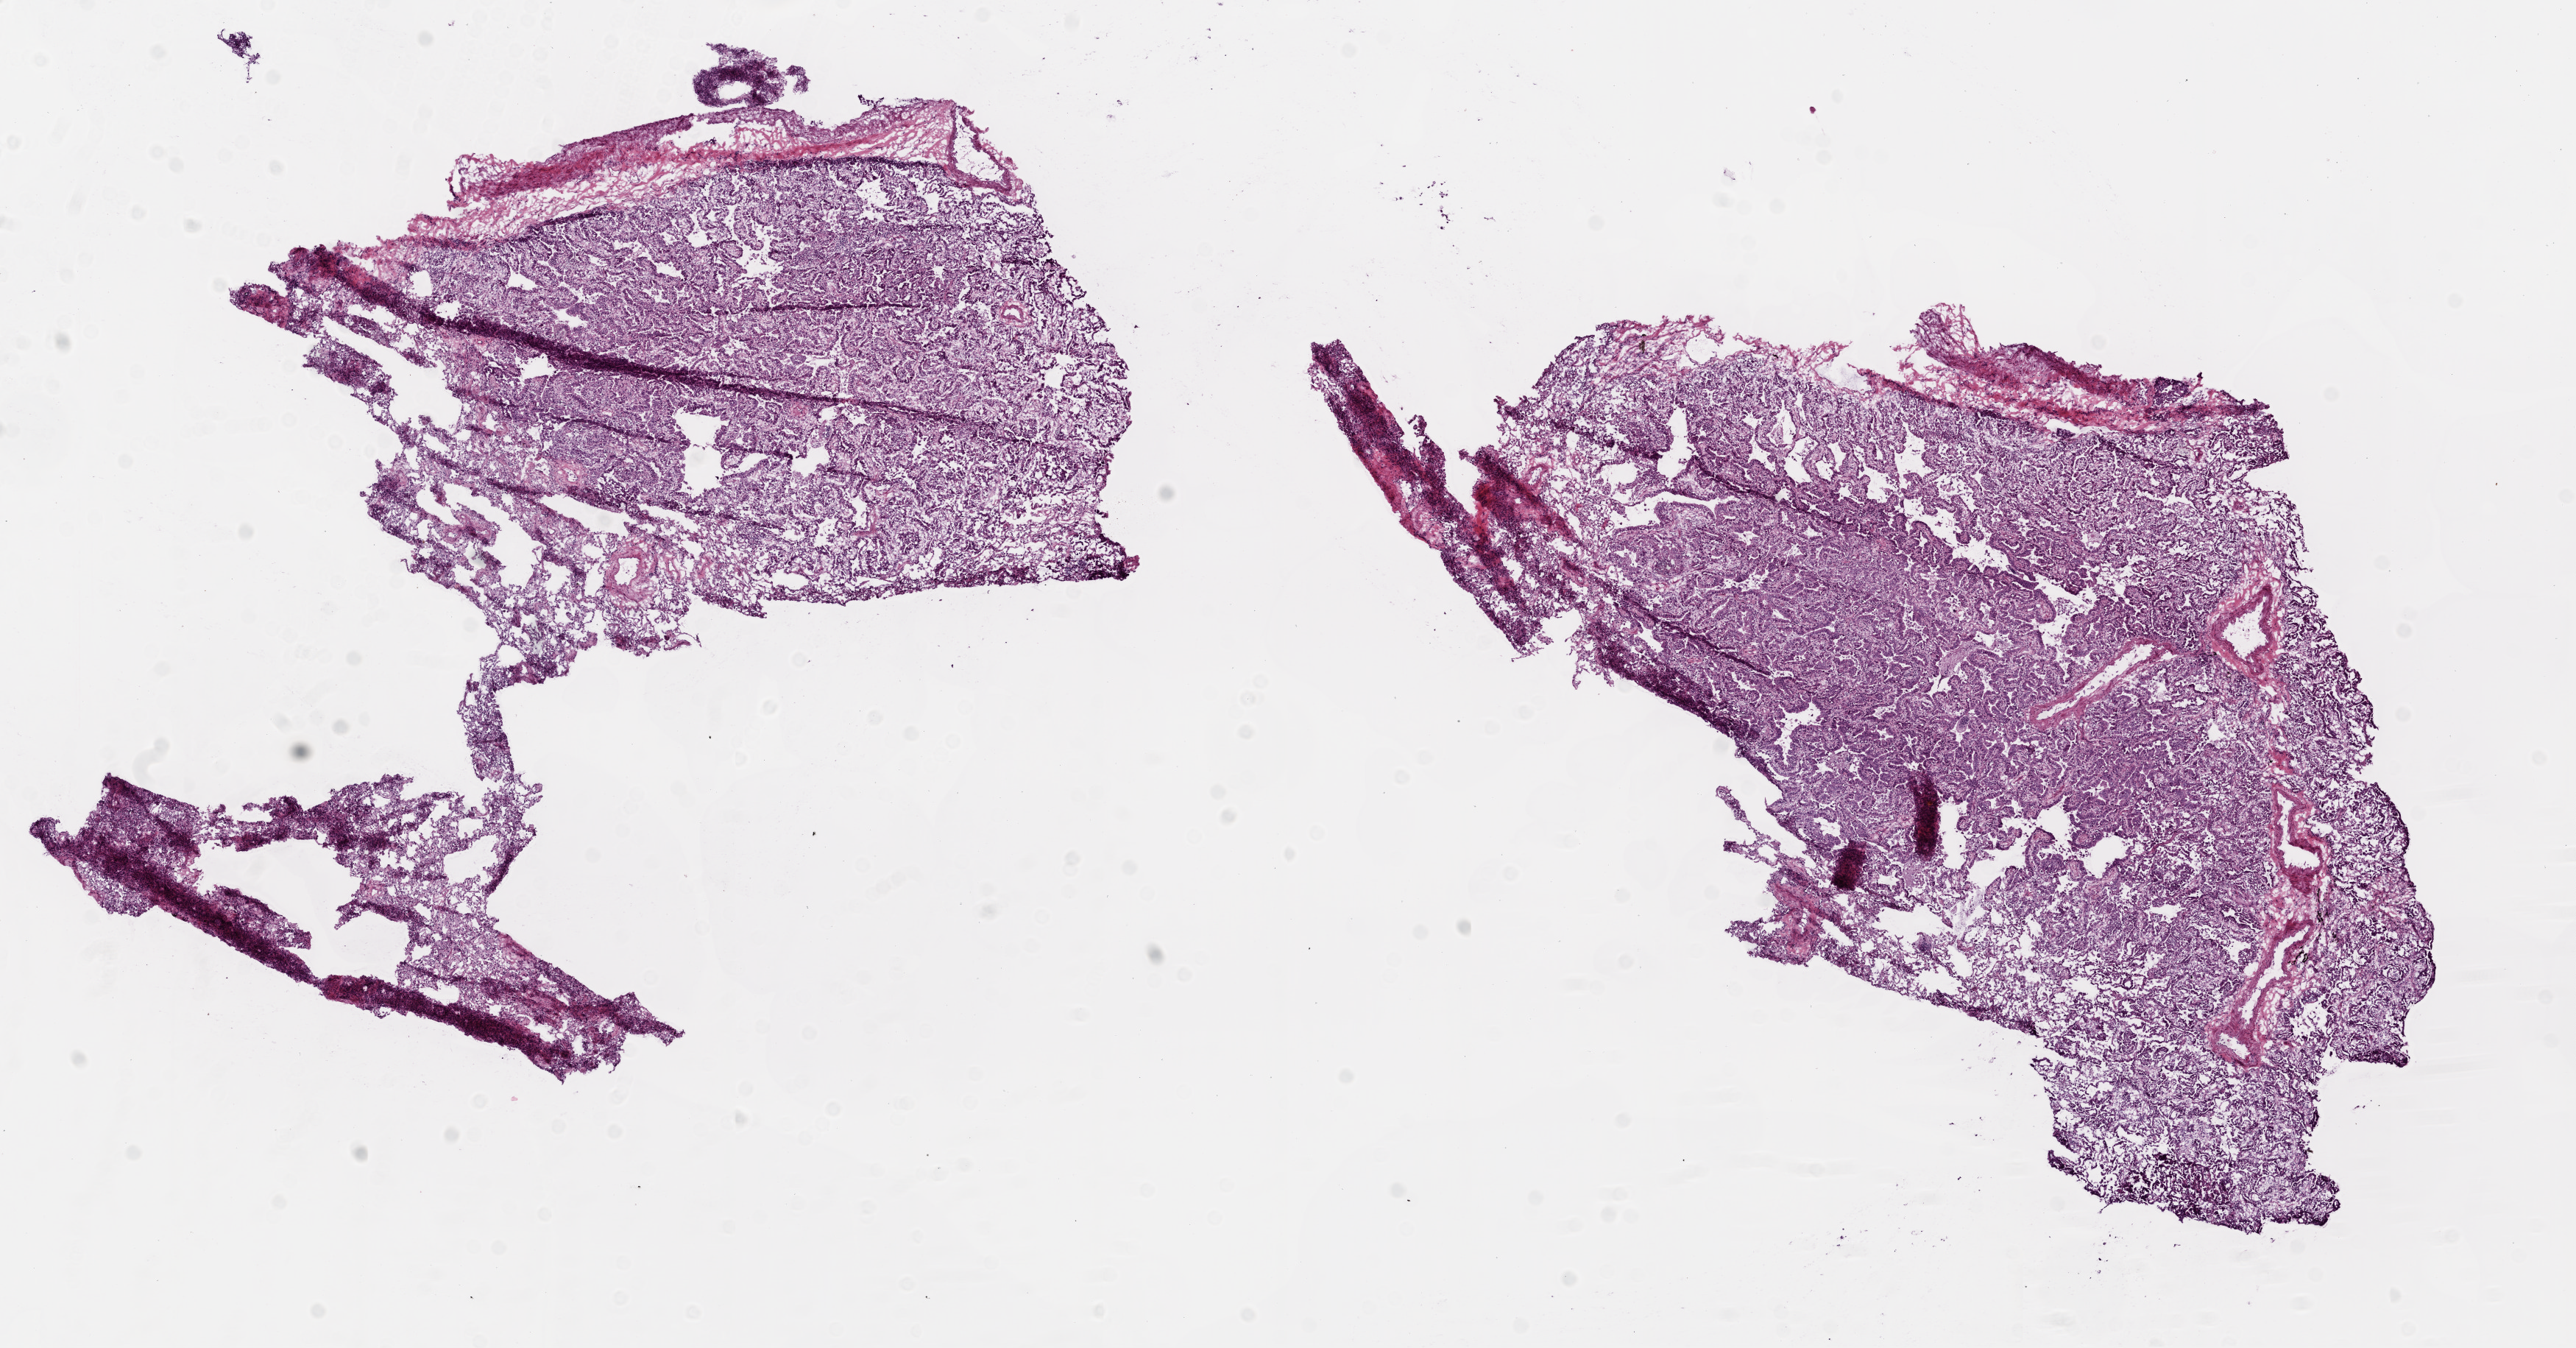
H&E whole-slide image, shown as a low-resolution overview of the whole scanned area (about 14.0 x 7.3 mm, from a 20x scan). Frozen section from the top of the tissue portion. Sample: primary tumour, lung. Male patient; age at initial diagnosis 66 years. Composition of this section per pathologist review: tumour cells 75%, tumour nuclei 70%, normal cells 15%, stromal cells 10%, necrosis 0%. Inflammatory infiltration, as recorded: lymphocyte infiltration 7%.
Laterality: right. Histologic diagnosis: Adenocarcinoma with mixed subtypes (lower lobe, lung). AJCC pathologic stage: IIIA (6th edition).